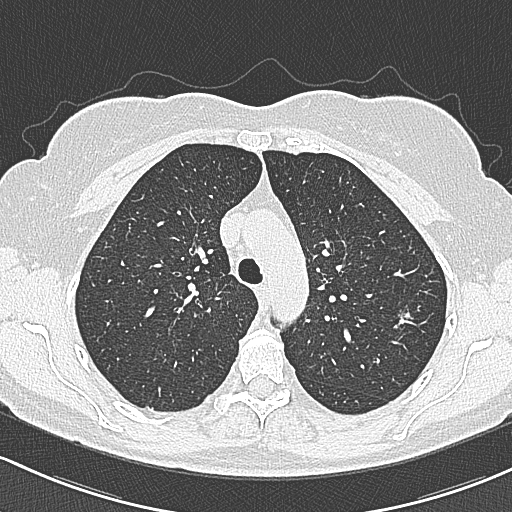
Chest CT (low-dose screening protocol), one axial image. Baseline annual screen. Lung window (W 1500 / L -600 HU). 120 kVp. 512 × 512 image matrix. Female, age 65 years at enrolment. Current smoker at enrolment.
Lesion marked by an expert reader, bounding box (x1, y1, x2, y2) in pixels: (379, 298, 422, 338). The screening reader recorded 3 non-calcified nodules or masses ≥4 mm on this exam (left upper lobe, left upper lobe, right upper lobe); which of them this box marks is not recorded. Official screen result: positive, change unspecified: nodule(s) >= 4 mm or enlarging nodule(s), mass(es), or other non-specific abnormalities suspicious for lung cancer. Participant outcome: lung cancer diagnosed 390 days after this screen — bronchiolo-alveolar carcinoma, non-mucinous, left upper lobe, stage IA (AJCC 6th edition), 10 mm at pathology.